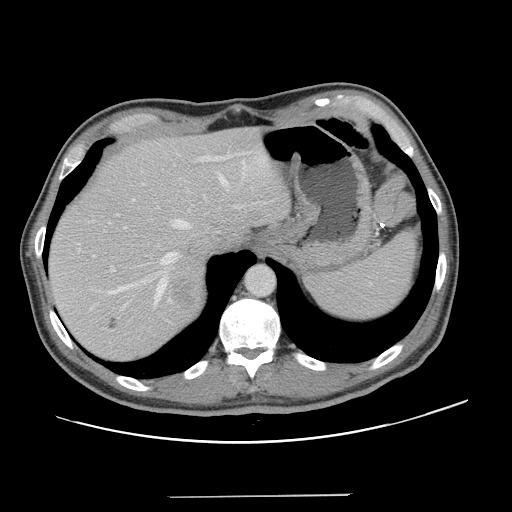
Contrast-enhanced abdominal CT, one axial slice; slice 104 of 131 in the series (ordered by position); 120 kVp; intravenous contrast given; soft-tissue window (W 400 / L 40 HU); 2.5 mm slice thickness; 512 × 512 image matrix, field of view 403 × 403 mm. Male patient, age 60 years. From the clinical record (not read from this slice): diagnosis: colorectal cancer liver metastases, imaged before liver resection; multiple liver metastases: no; largest metastasis: 2.5 cm.
Annotated regions visible in this slice (manually delineated by an expert):
- hepatic veins: bounding box (x1, y1, x2, y2) in pixels: (107, 173, 228, 307)
- liver: (48, 128, 290, 361)
- planned liver remnant (the part of the liver to remain after resection): (48, 128, 290, 350)
- portal vein (with intrahepatic branches): (92, 155, 260, 272)
- liver metastasis: (169, 281, 201, 311)